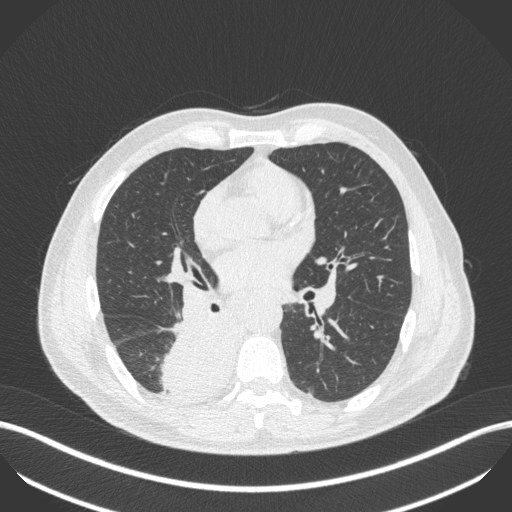
Chest CT, one axial slice; slice 243 of 451 in the series (ordered by position); reconstruction kernel B31f; 100 kVp; lung window (W 1500 / L -600 HU); 1 mm slice thickness; 512 × 512 image matrix, field of view 400 × 400 mm. Patient: male, 61 years. Case-level facts recorded for this patient, not image findings: clinical TNM (as recorded): T1 N0 M0.
Annotated regions visible in this slice (bounding box drawn by a radiologist):
- lung tumour (recorded histology: small cell carcinoma): bounding box (x1, y1, x2, y2) in pixels: (160, 303, 238, 397)